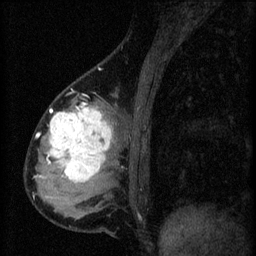
Breast MRI (dynamic contrast-enhanced), one sagittal slice; slice 19 of 60 in the series (ordered by position); 3 images stored at this slice position (order not interpretable as contrast timing); 1.5 T; TE 4.2 ms, TR 8.2 ms; 2 mm slice thickness; 256 × 256 image matrix, field of view 180 × 180 mm. Female patient, age 37 years.
Outlined on this slice (semi-automatic segmentation, software-assisted and operator-edited):
- analysis volume of interest (the breast-tissue region the enhancement analysis was run in; not a lesion): box from (x=44, y=100) to (x=119, y=197) px
- tumour enhancement mask (voxels above the 70 % enhancement threshold inside the analysis volume of interest): (x=48, y=106)–(x=113, y=183)